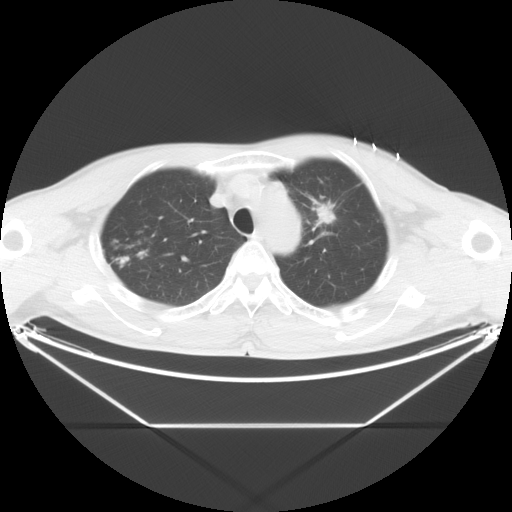
Chest CT, one axial slice. Slice 22 of 26 in the series (ordered by position). Reconstruction kernel STANDARD. Lung window (W 1500 / L -600 HU). 512 × 512 image matrix, field of view 443 × 443 mm. Male patient, age 60 years. Case-level facts recorded for this patient, not image findings: clinical TNM (as recorded): T2 N1 M0.
Annotated regions visible in this slice (bounding box drawn by a radiologist):
- lung tumour (recorded histology: adenocarcinoma): bounding box [x1, y1, x2, y2] px = [313, 201, 337, 227]